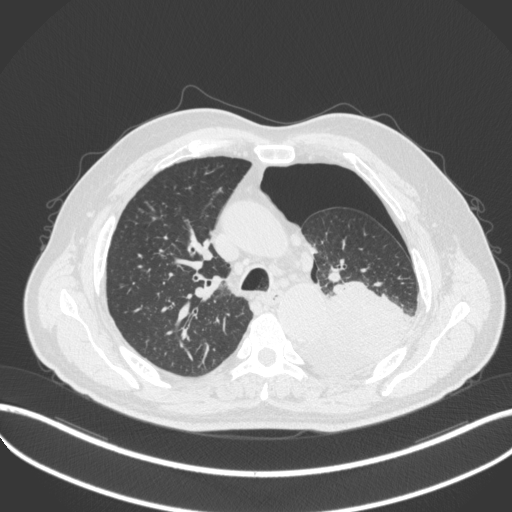
Chest CT, one axial slice. Position 355 of 466 along the scan axis. Reconstruction kernel B31f. 120 kVp. Lung window (W 1500 / L -600 HU). 1 mm slice thickness. 512 × 512 image matrix, field of view 400 × 400 mm. Male patient, age 76 years. Case-level facts recorded for this patient, not image findings: clinical TNM (as recorded): T3 N0 M1b.
Annotated regions visible in this slice (bounding box drawn by a radiologist):
- lung tumour (recorded histology: adenocarcinoma): bounding box (x1, y1, x2, y2) in pixels: (289, 278, 420, 379)